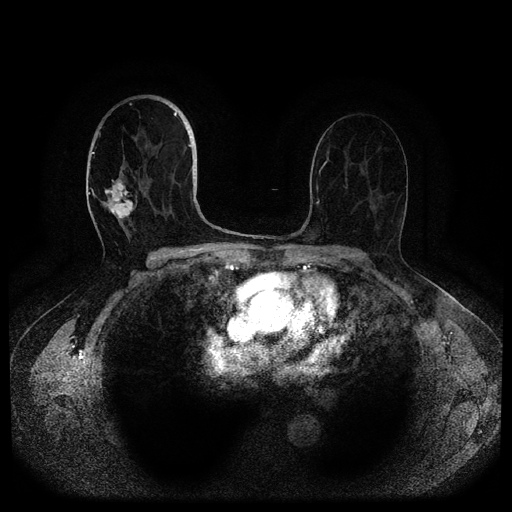
Breast MRI (dynamic contrast-enhanced, multi-phase), one axial slice; position 59 of 116 along the scan axis; dynamic contrast-enhanced series, time point 2 of 5 at this slice position (early post-contrast); 1.5 T; TE 2.6 ms, TR 5.3 ms; 2 mm slice thickness; 512 × 512 image matrix, field of view 350 × 350 mm. Patient: female, 82 years.
Outlined on this slice (semi-automatically segmented with operator editing):
- breast lesion (labelled 'tumour' in the annotation; benign lesions carry a separate 'benign' label): box from (x=103, y=178) to (x=137, y=221) px